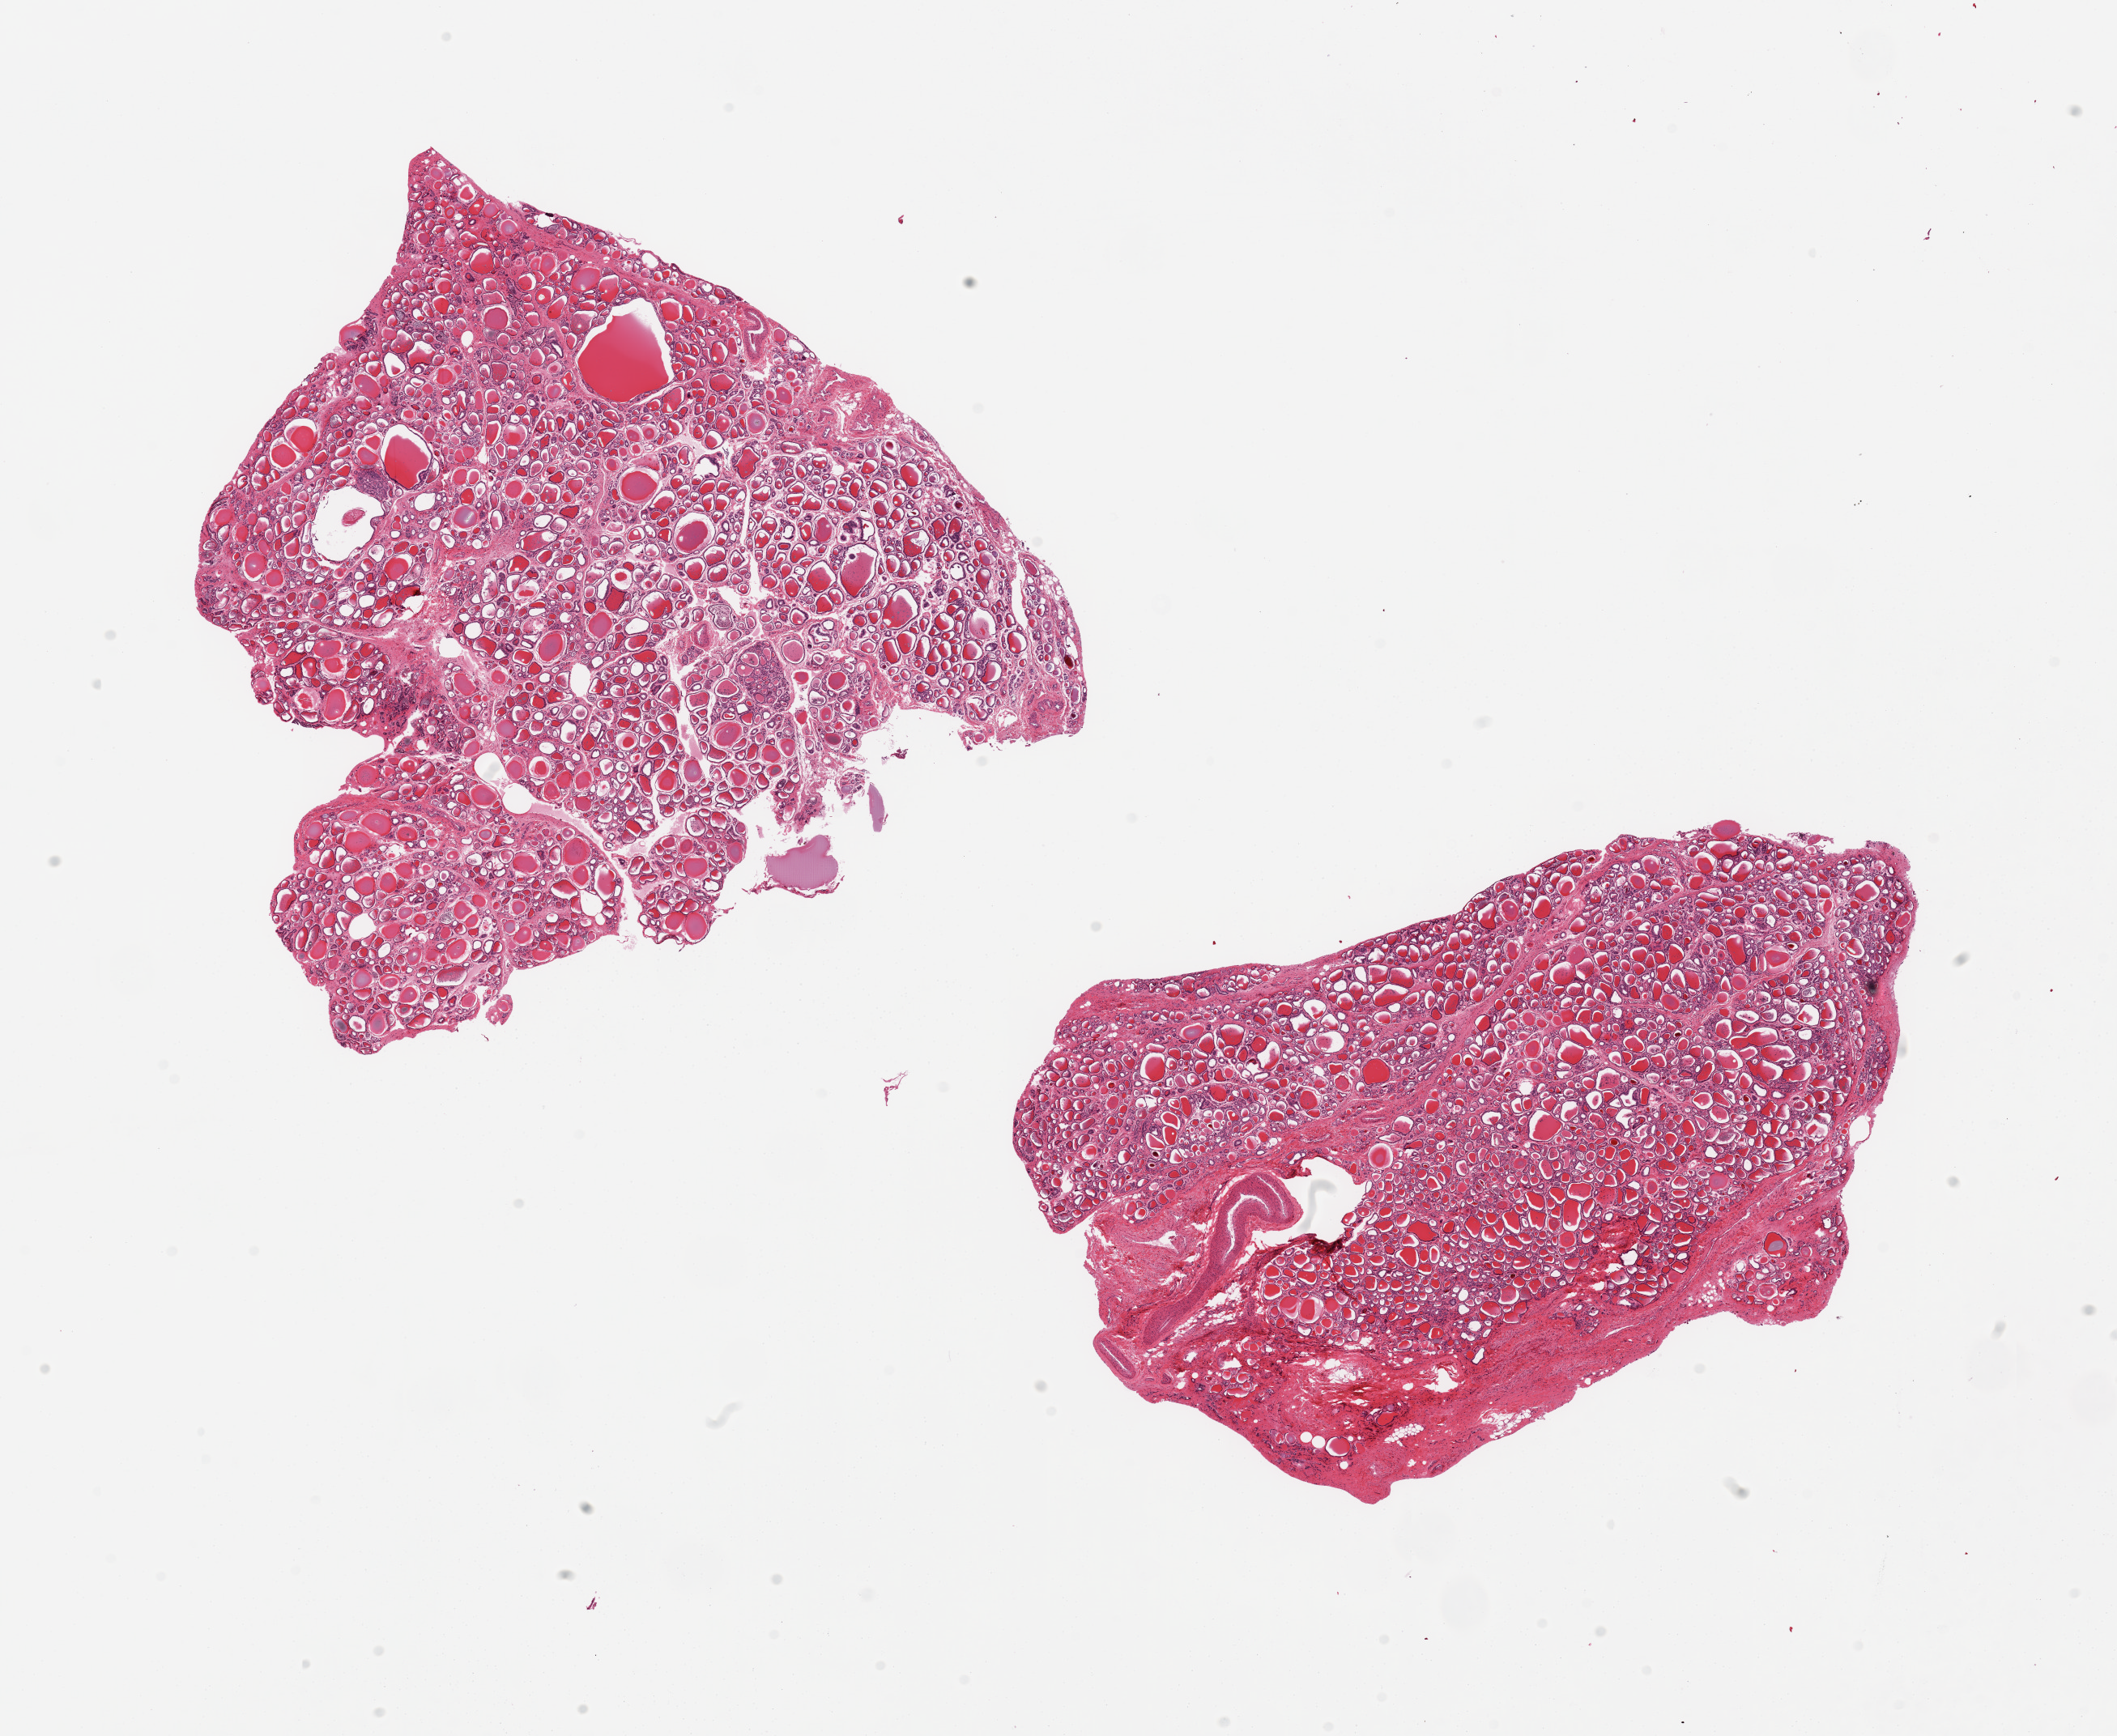
Digitized H&E-stained section, a low-resolution overview of the entire scanned area, about 20.7 x 17.0 mm, PAXgene-fixed paraffin-embedded (PFPE) section, section of thyroid (target tissue), donor tissue sample. Donor sex: female.
Pathologist's review note for this sample: 2 pieces, one piece is ~30% fibrous tissue and large vessels.